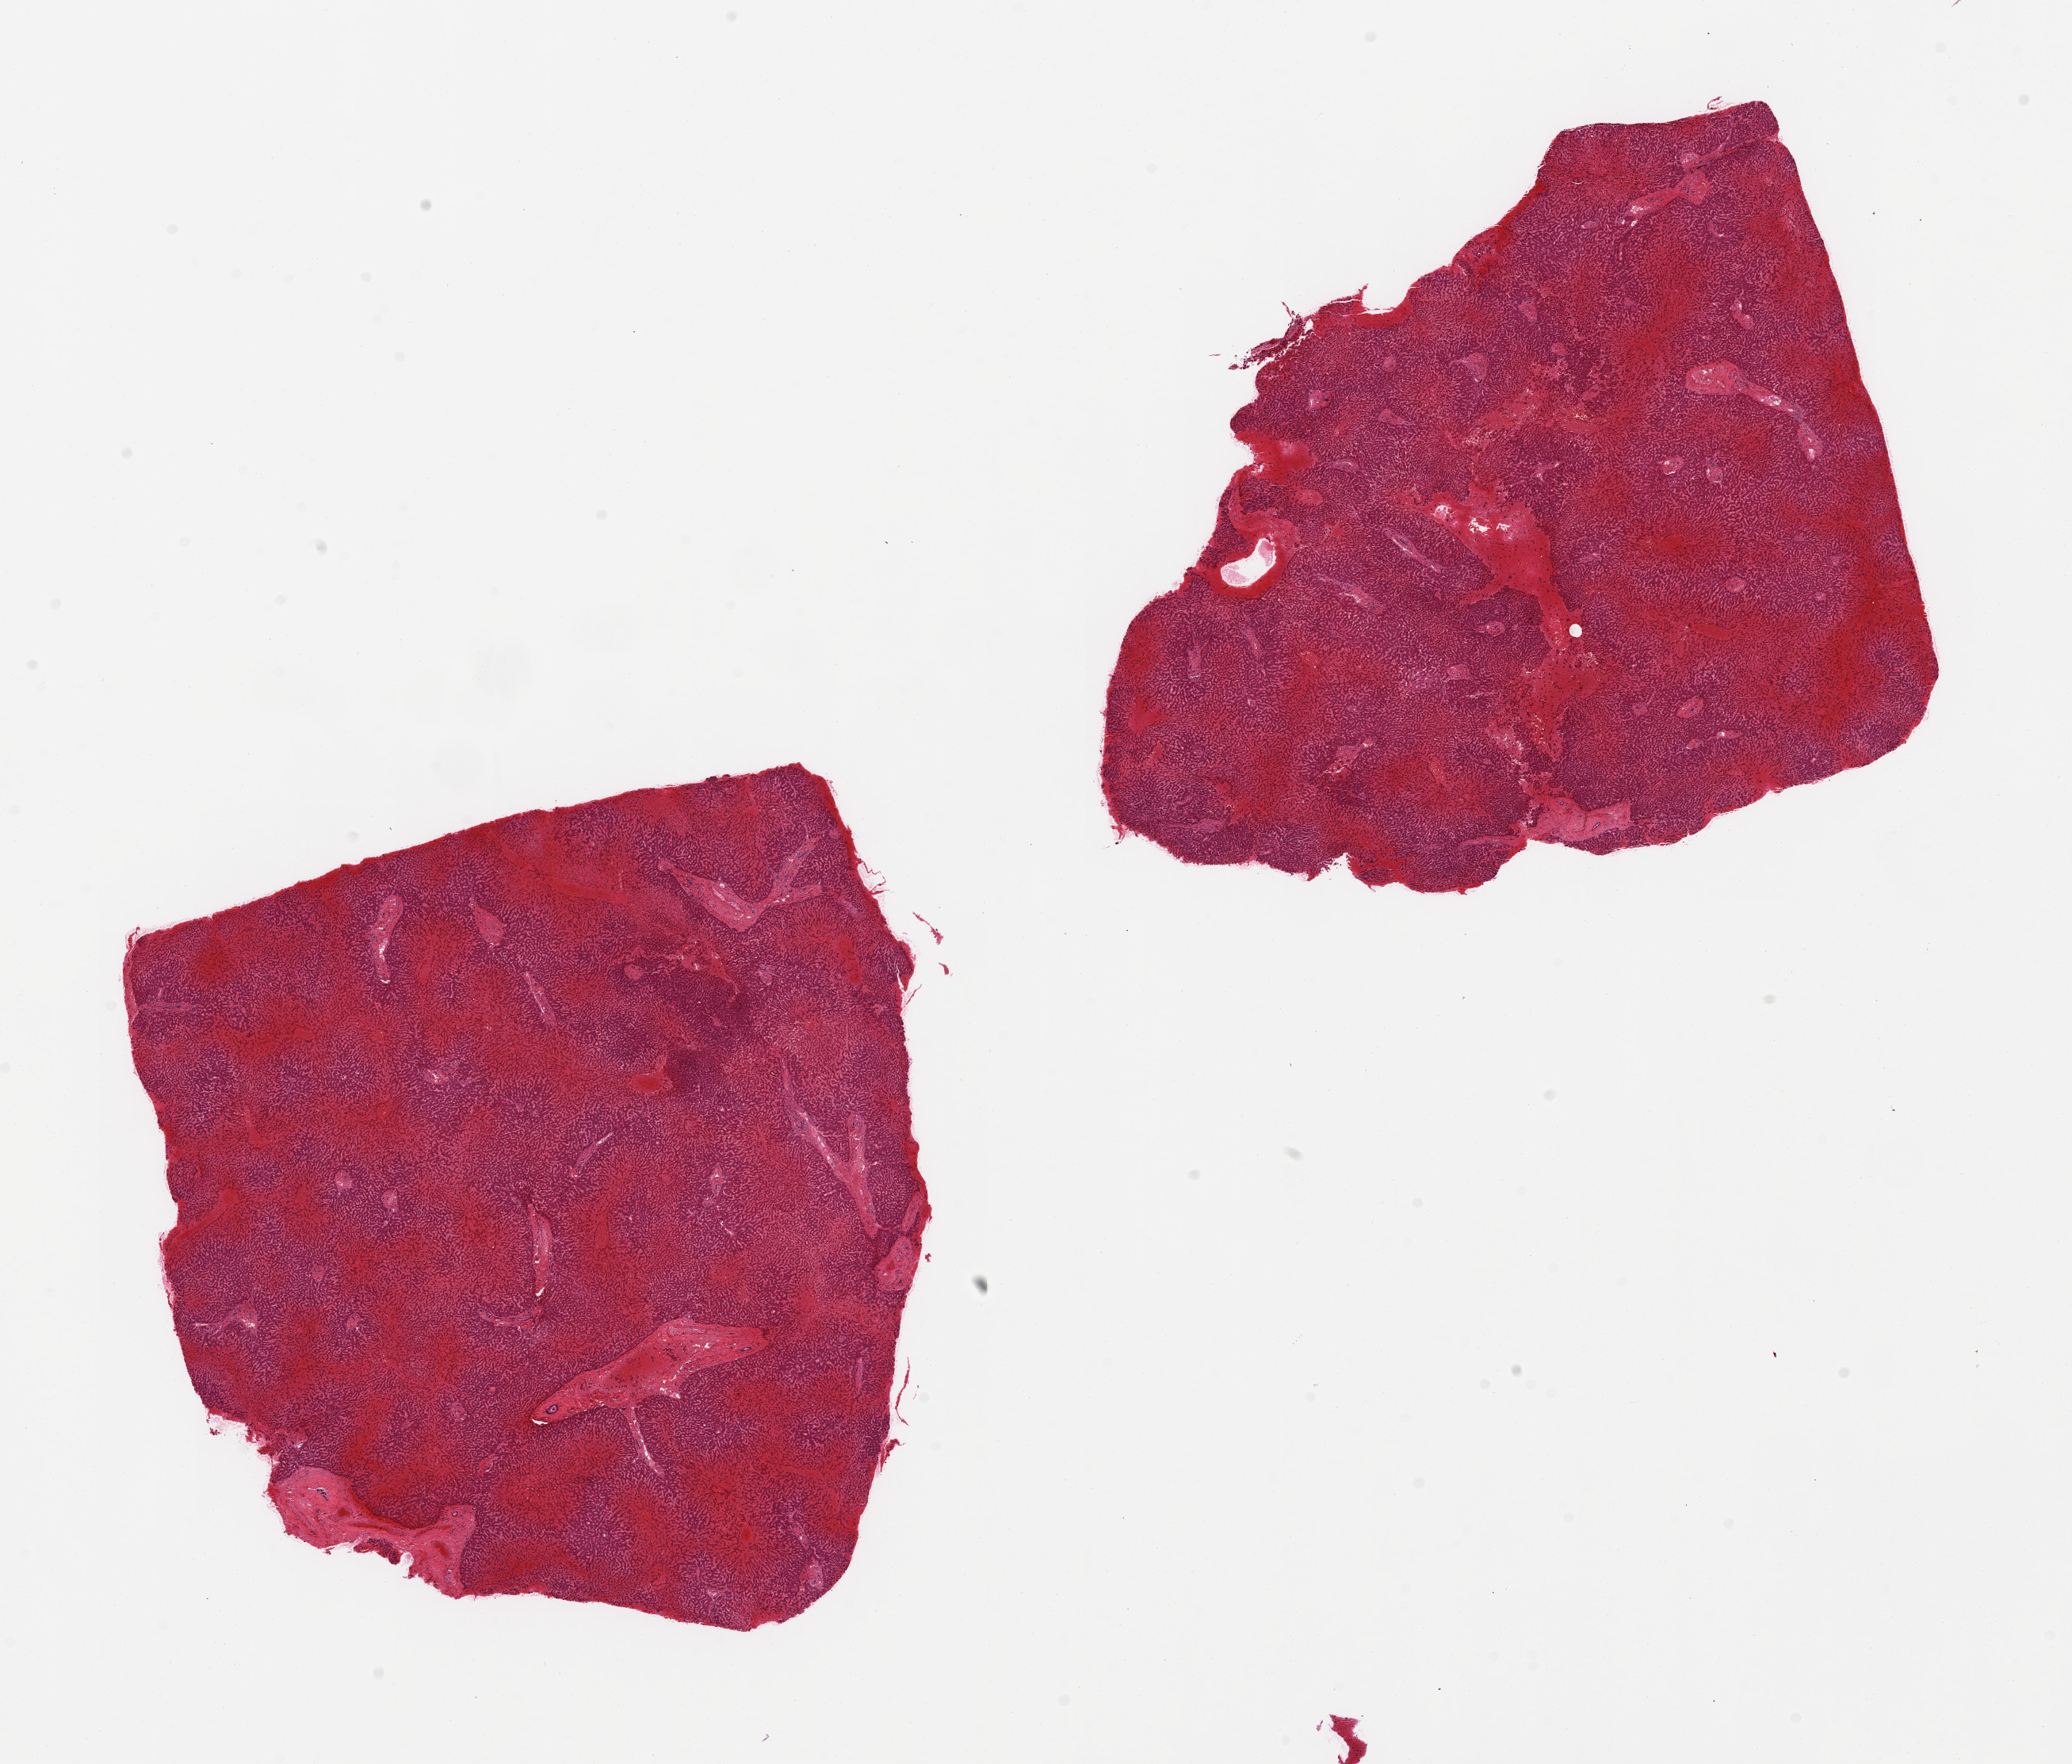
Haematoxylin and eosin whole-slide image, shown as a low-resolution overview of the whole scanned area (about 20.7 x 17.6 mm). PAXgene-fixed, paraffin-embedded tissue. Target tissue: liver. Donor tissue sample. Donor: male.
Reviewer comment on this tissue sample: 2 pieces severe acute congestion/hemorrhagic infarction.